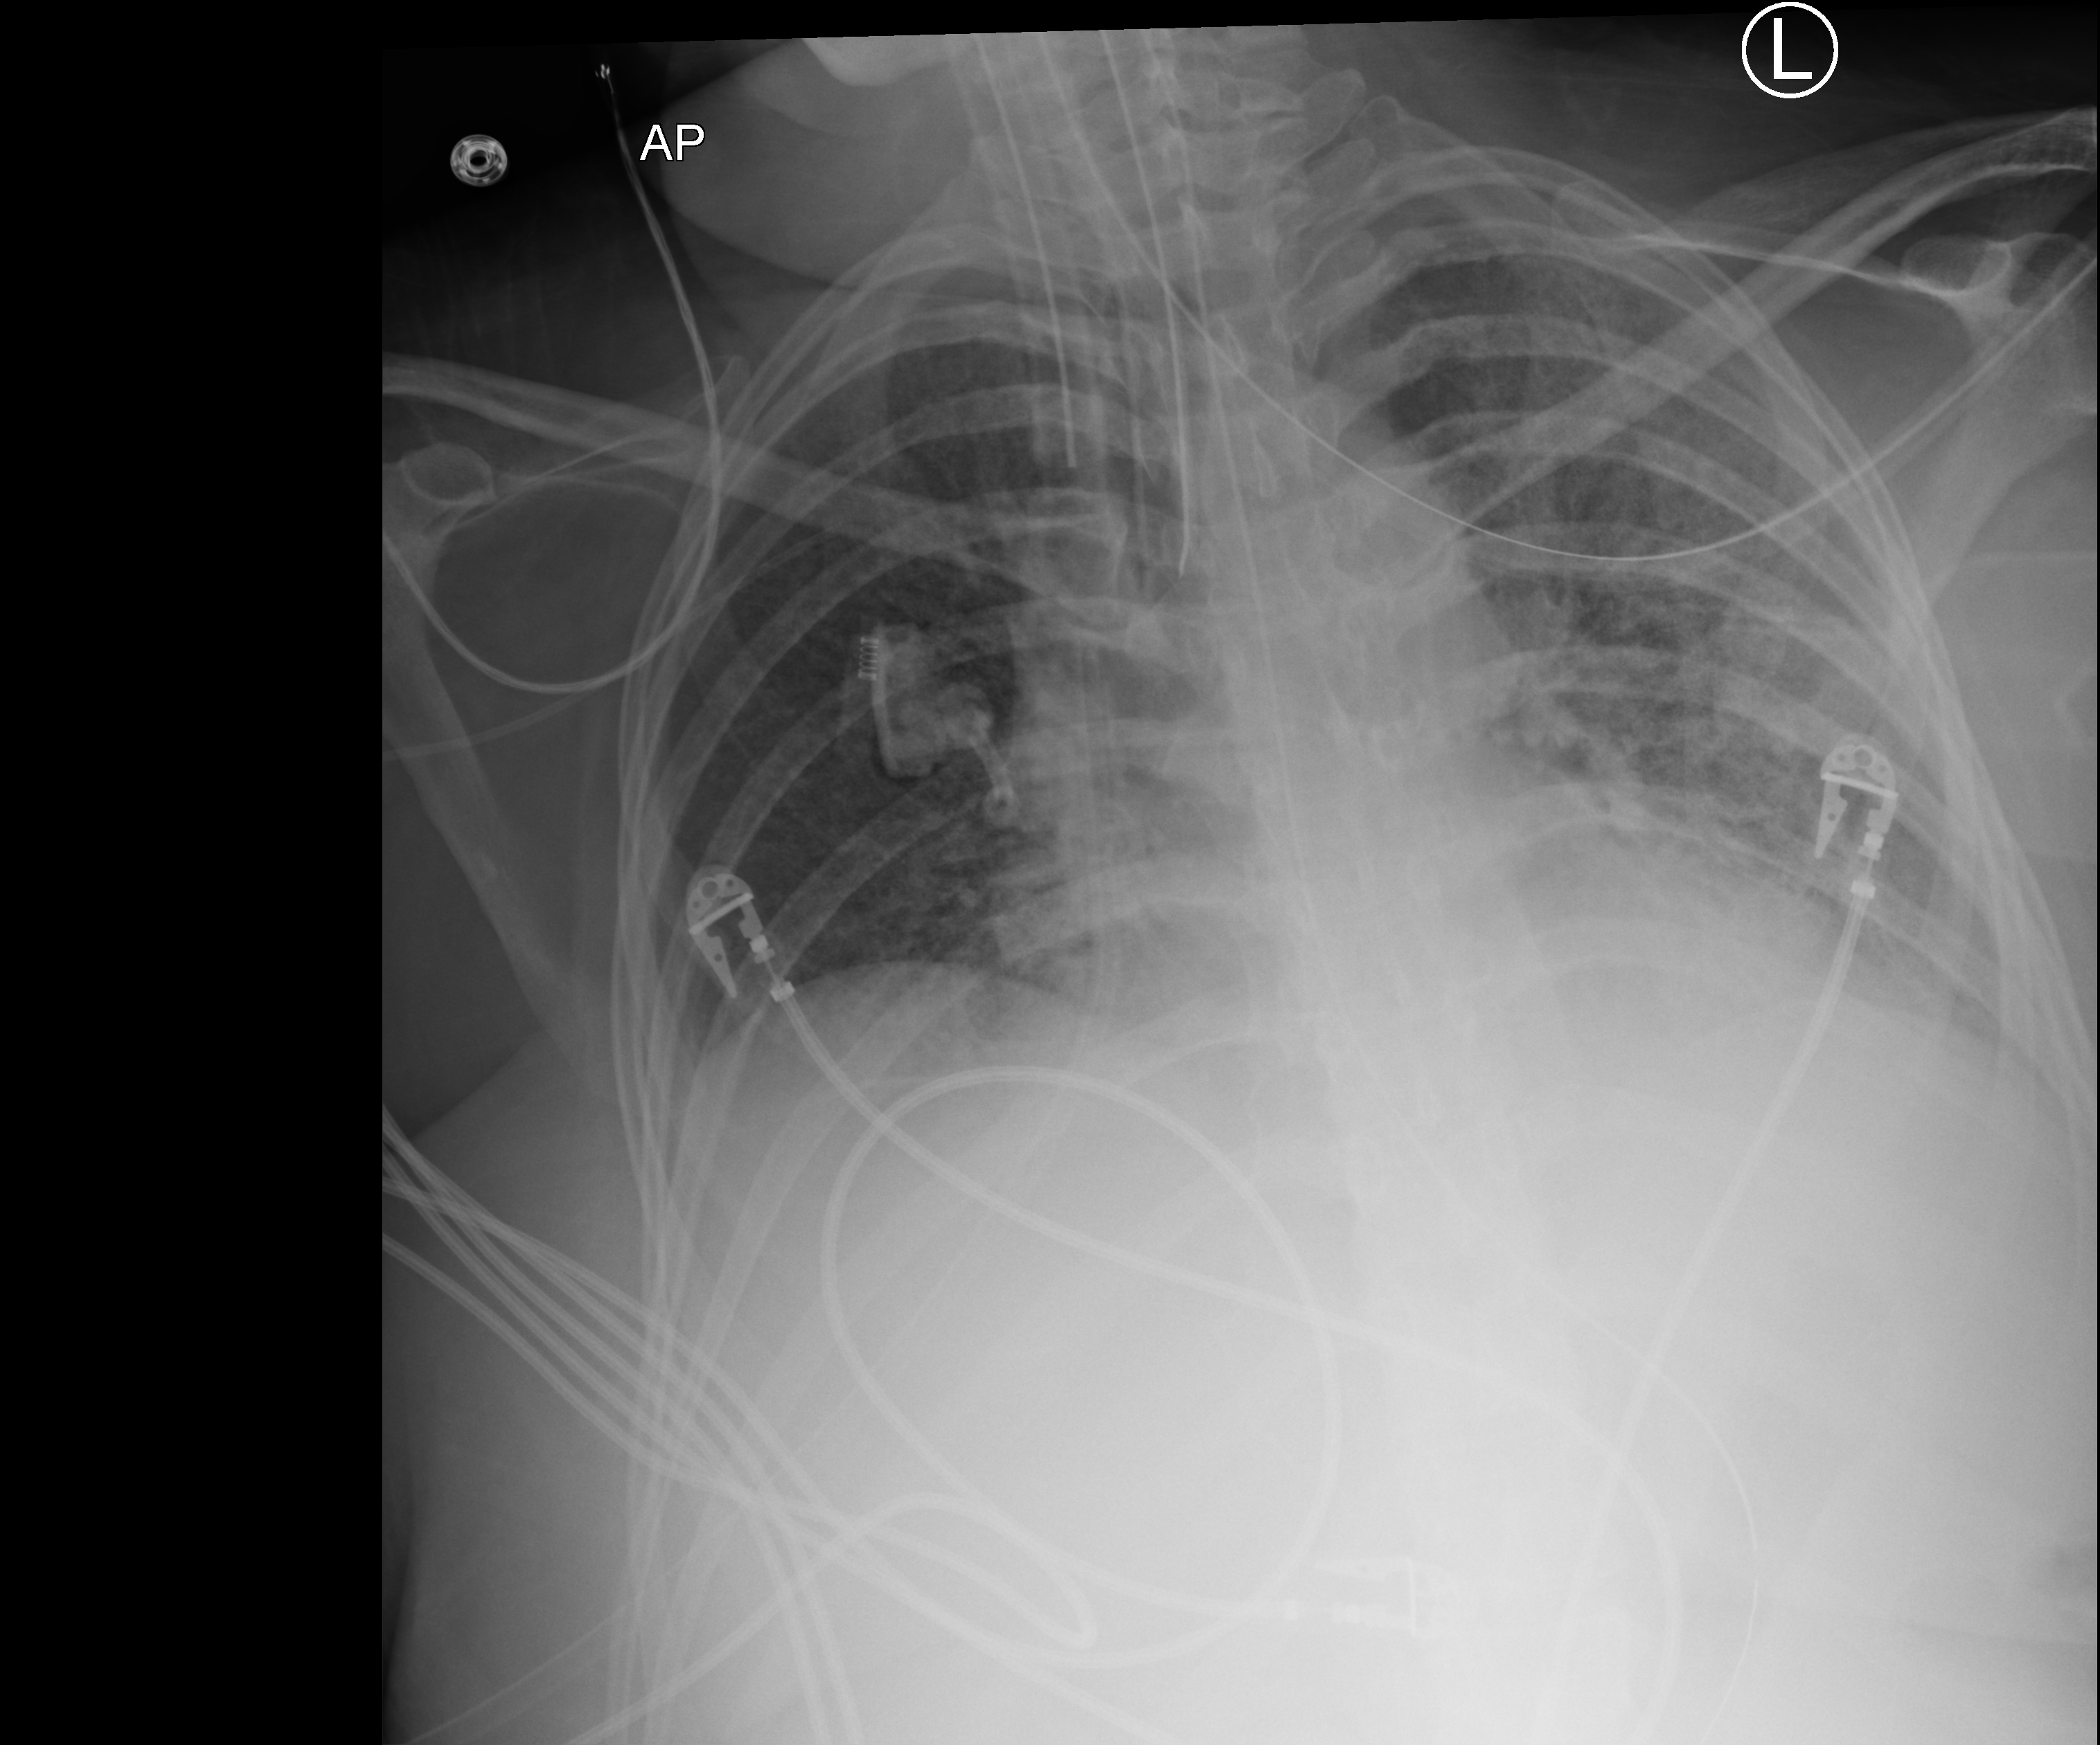
Portable chest radiograph, anteroposterior (AP) projection. Patient hospitalised with COVID-19; female, aged 18–59 years.
Admission-level facts for this patient (not findings on this image; timing relative to this image not recorded): mechanically ventilated during this hospital stay: yes.